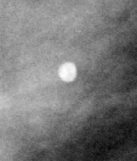
Region of interest cut from a scanned film mammogram (one marked finding); right breast; MLO view.
Marked abnormality: calcifications, morphology round and regular; BI-RADS assessment category 2; benign; no additional work-up was recommended (benign without callback).